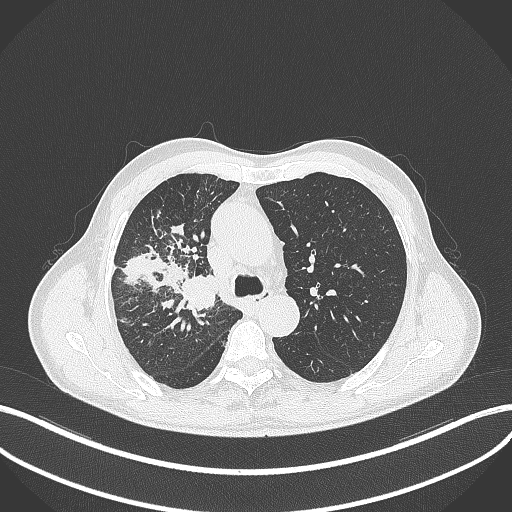
Chest CT, one axial slice; slice 333 of 490 in the series (ordered by position); reconstruction kernel B70f; lung window (W 1500 / L -600 HU); 1 mm slice thickness; 512 × 512 image matrix, field of view 400 × 400 mm. Patient: male, 69 years. Case-level facts recorded for this patient, not image findings: clinical TNM (as recorded): T2a N0 M0.
Annotated regions visible in this slice (rectangle marked by the reading radiologist):
- lung tumour (recorded histology: adenocarcinoma): bounding box (x1, y1, x2, y2) in pixels: (179, 274, 219, 312)